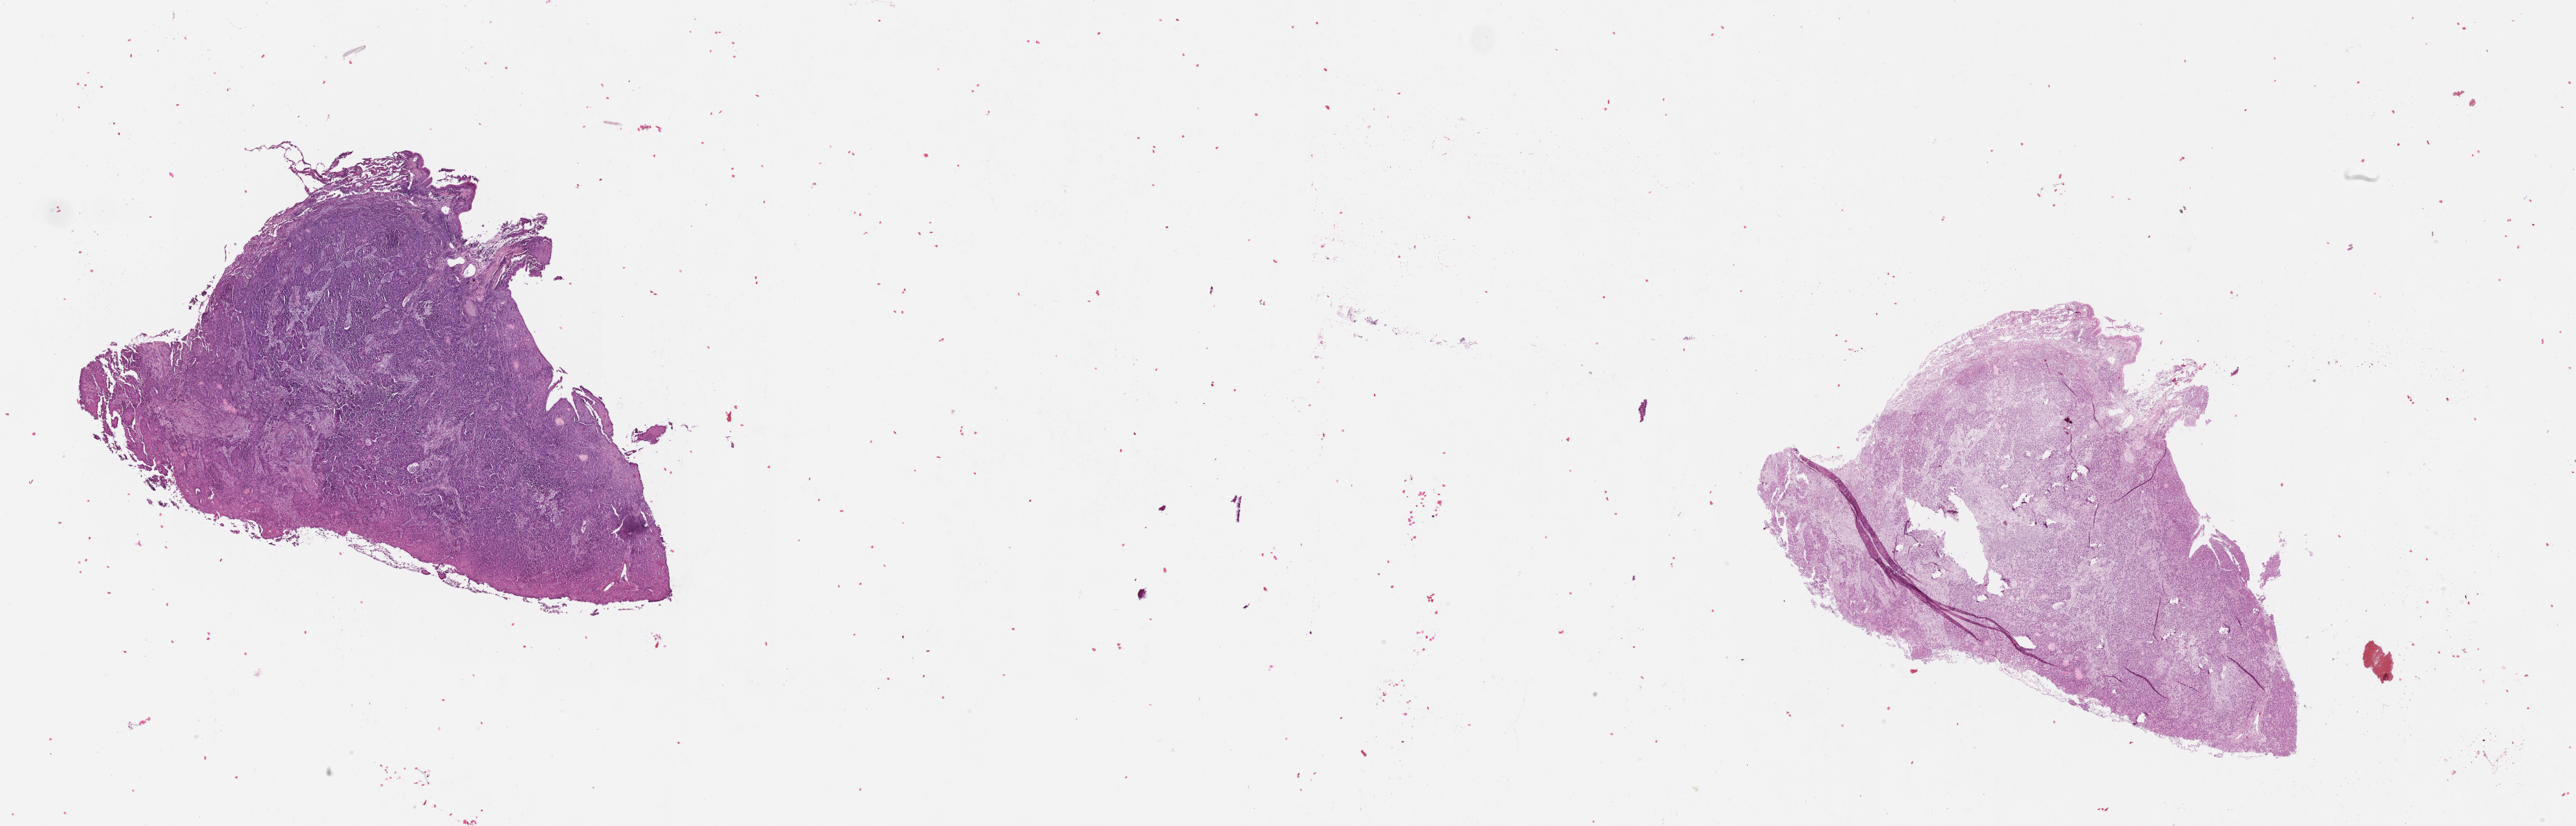
Whole-slide histology image, H&E, a low-resolution overview of the entire scanned area, about 30.1 x 9.6 mm, lung, tumour tissue. Female, 70 y/o.
Patient diagnosis (cohort enrolment): squamous cell carcinoma (lung).